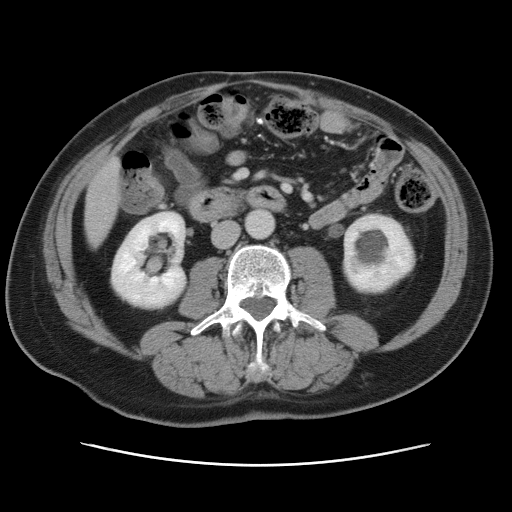
Contrast-enhanced abdominal CT, one axial slice; position 16 of 80 along the scan axis; 120 kVp; soft-tissue window (W 400 / L 40 HU); 5 mm slice thickness; 512 × 512 image matrix. Male patient, age 69 years. From the clinical record (not read from this slice): diagnosis: colorectal cancer liver metastases, imaged before liver resection; multiple liver metastases: no; largest metastasis: 5 cm; chemotherapy before resection: no.
Outlined on this slice (outlined manually by an expert reader):
- liver: bounding box [x1, y1, x2, y2] px = [85, 161, 119, 244]
- planned liver remnant (the part of the liver to remain after resection): [87, 227, 108, 243]